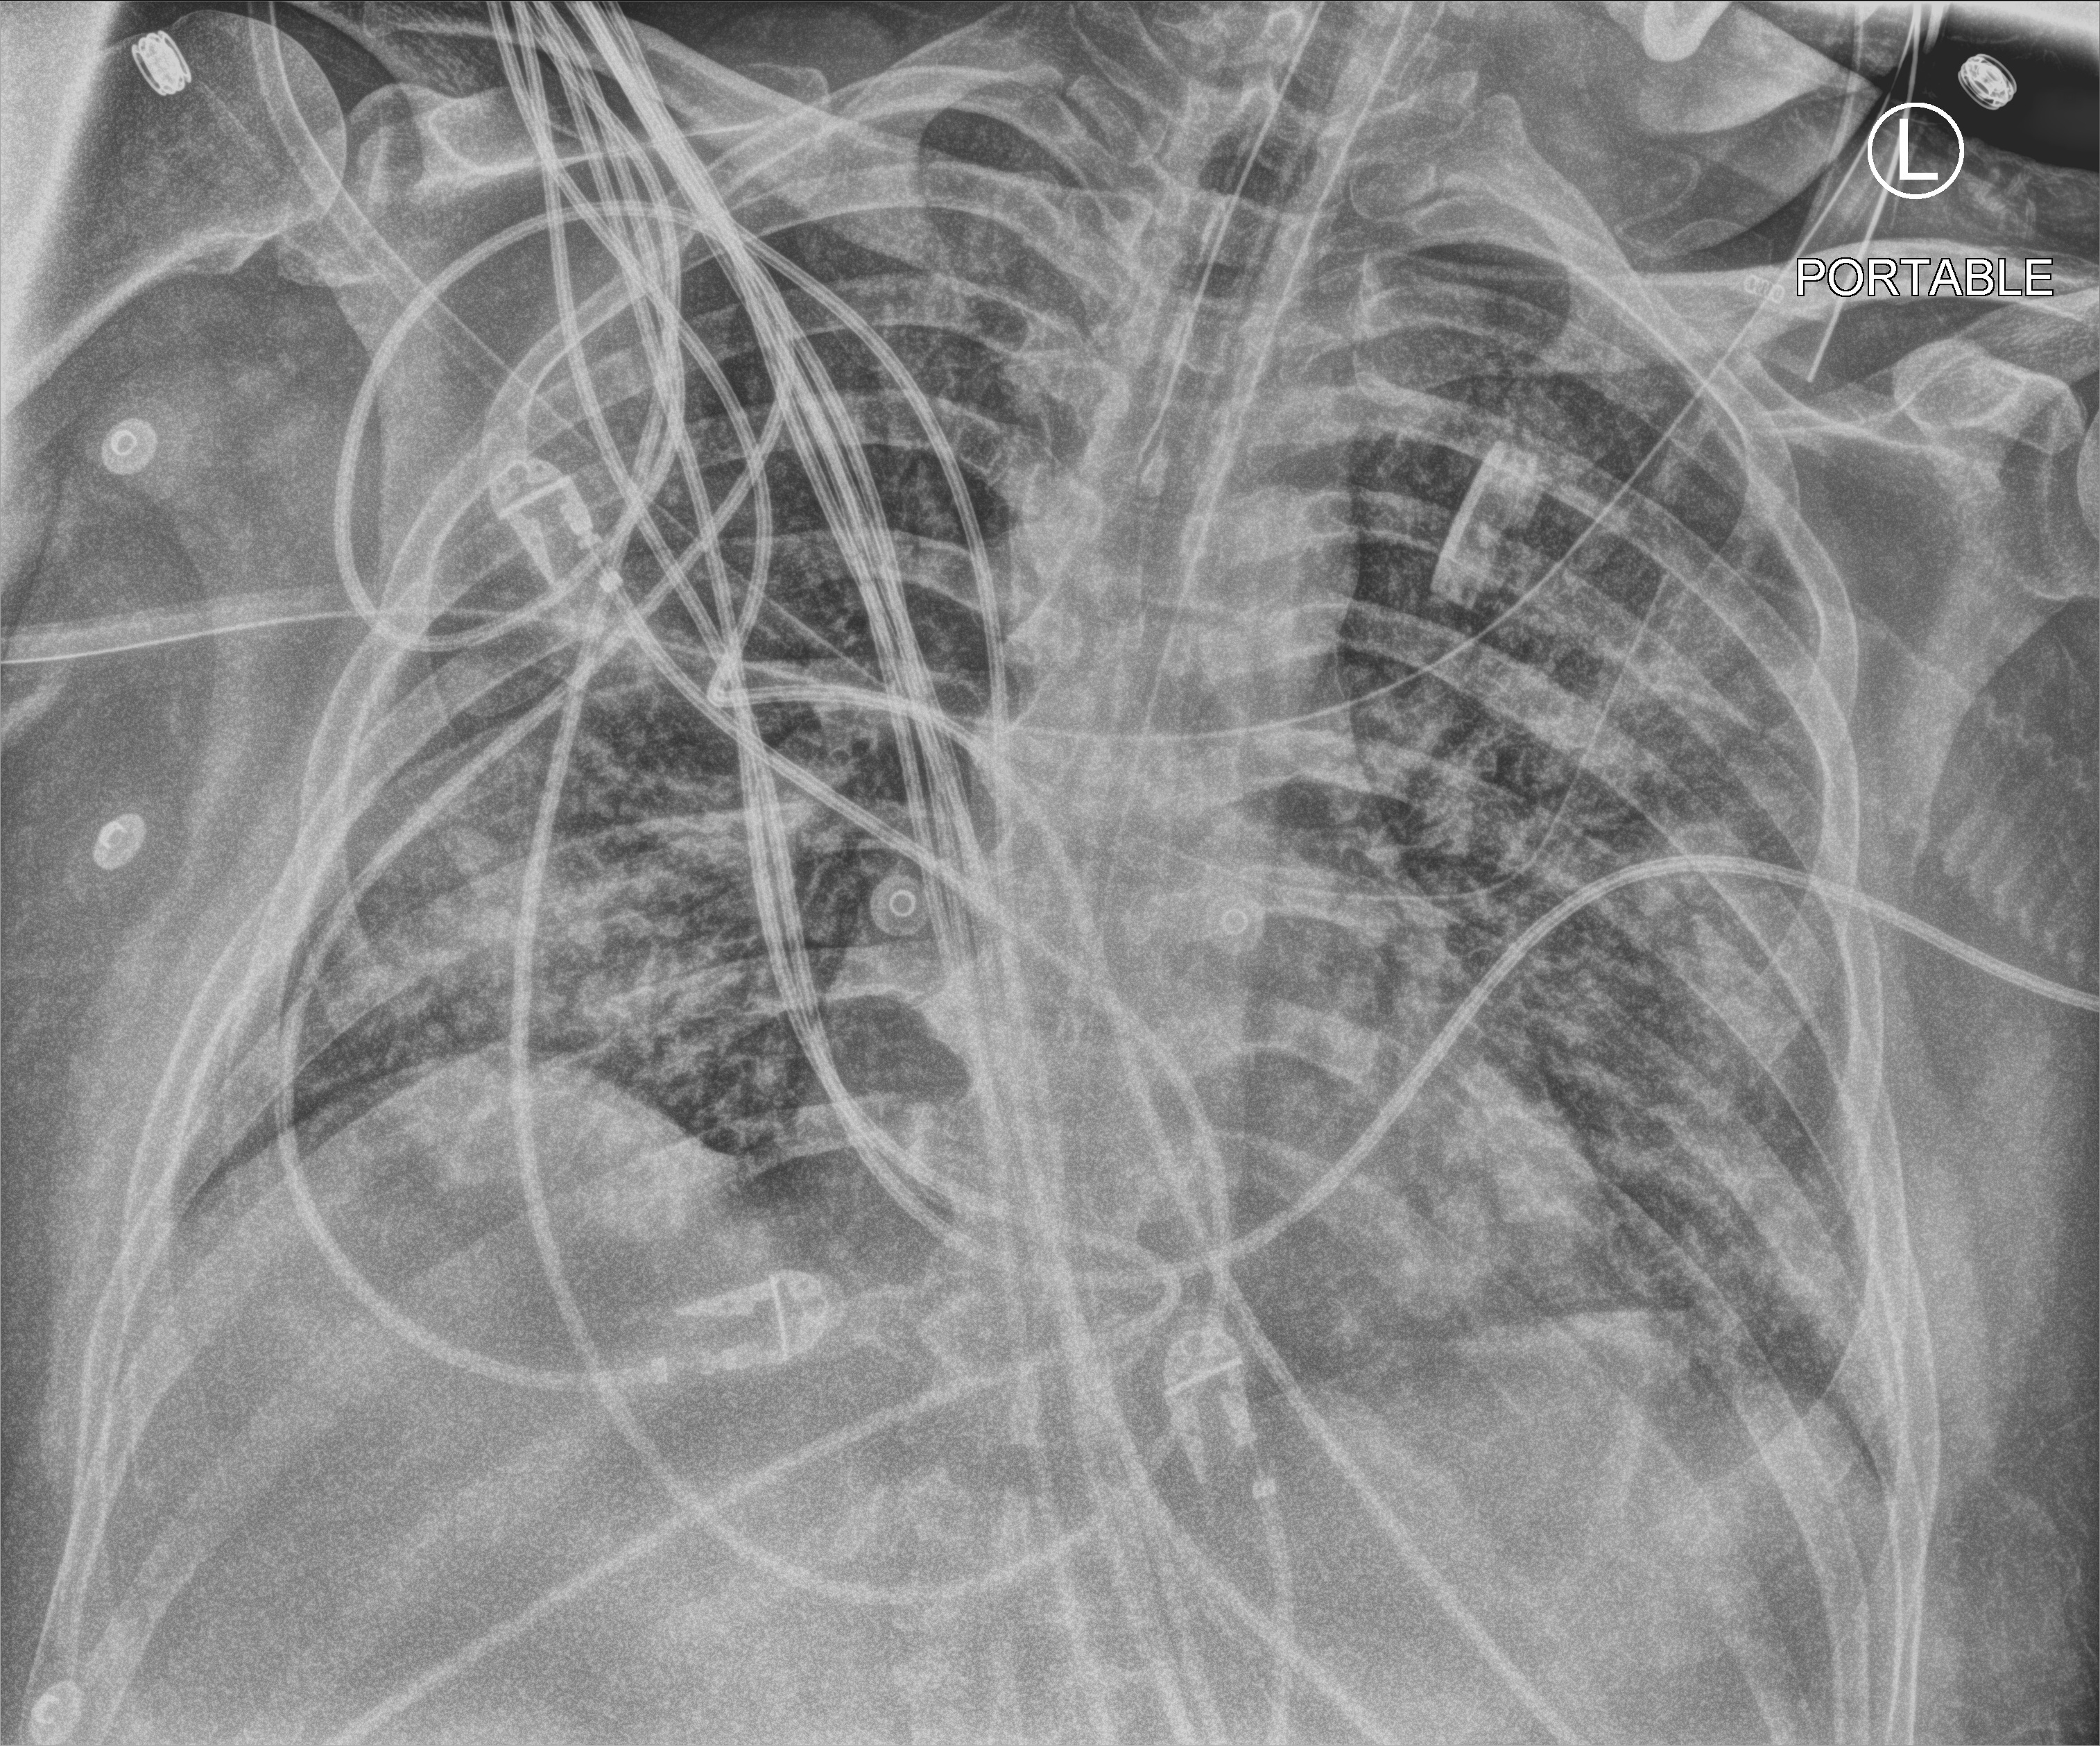
Bedside chest radiograph (computed radiography), anteroposterior (AP) projection. Patient hospitalised with COVID-19; male, aged 18–59 years.
Hospital-stay facts (about this admission, not read from this image; timing relative to this image not recorded):
- other chronic lung disease (admission record): no